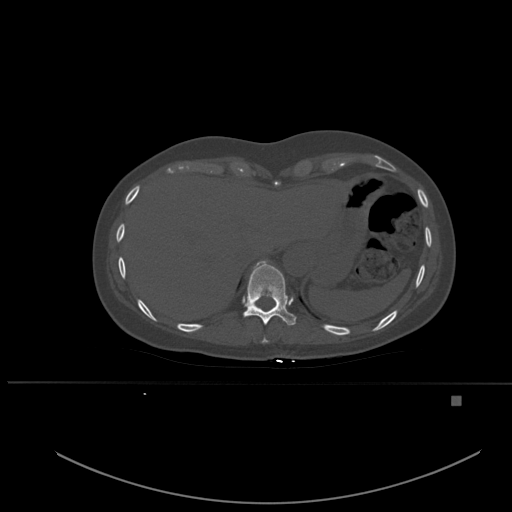
CT including the spine, one axial slice. Bone window (W 1800 / L 400 HU). 512 × 512 image matrix, field of view 443 × 443 mm. Female patient, age 49 years. From the clinical record (not read from this slice): primary cancer: breast.
Annotated regions visible in this slice (semi-automatically segmented with operator editing):
- T10 vertebra: box from (x=243, y=261) to (x=296, y=326) px
- T9 vertebra: (x=261, y=337)–(x=269, y=343)